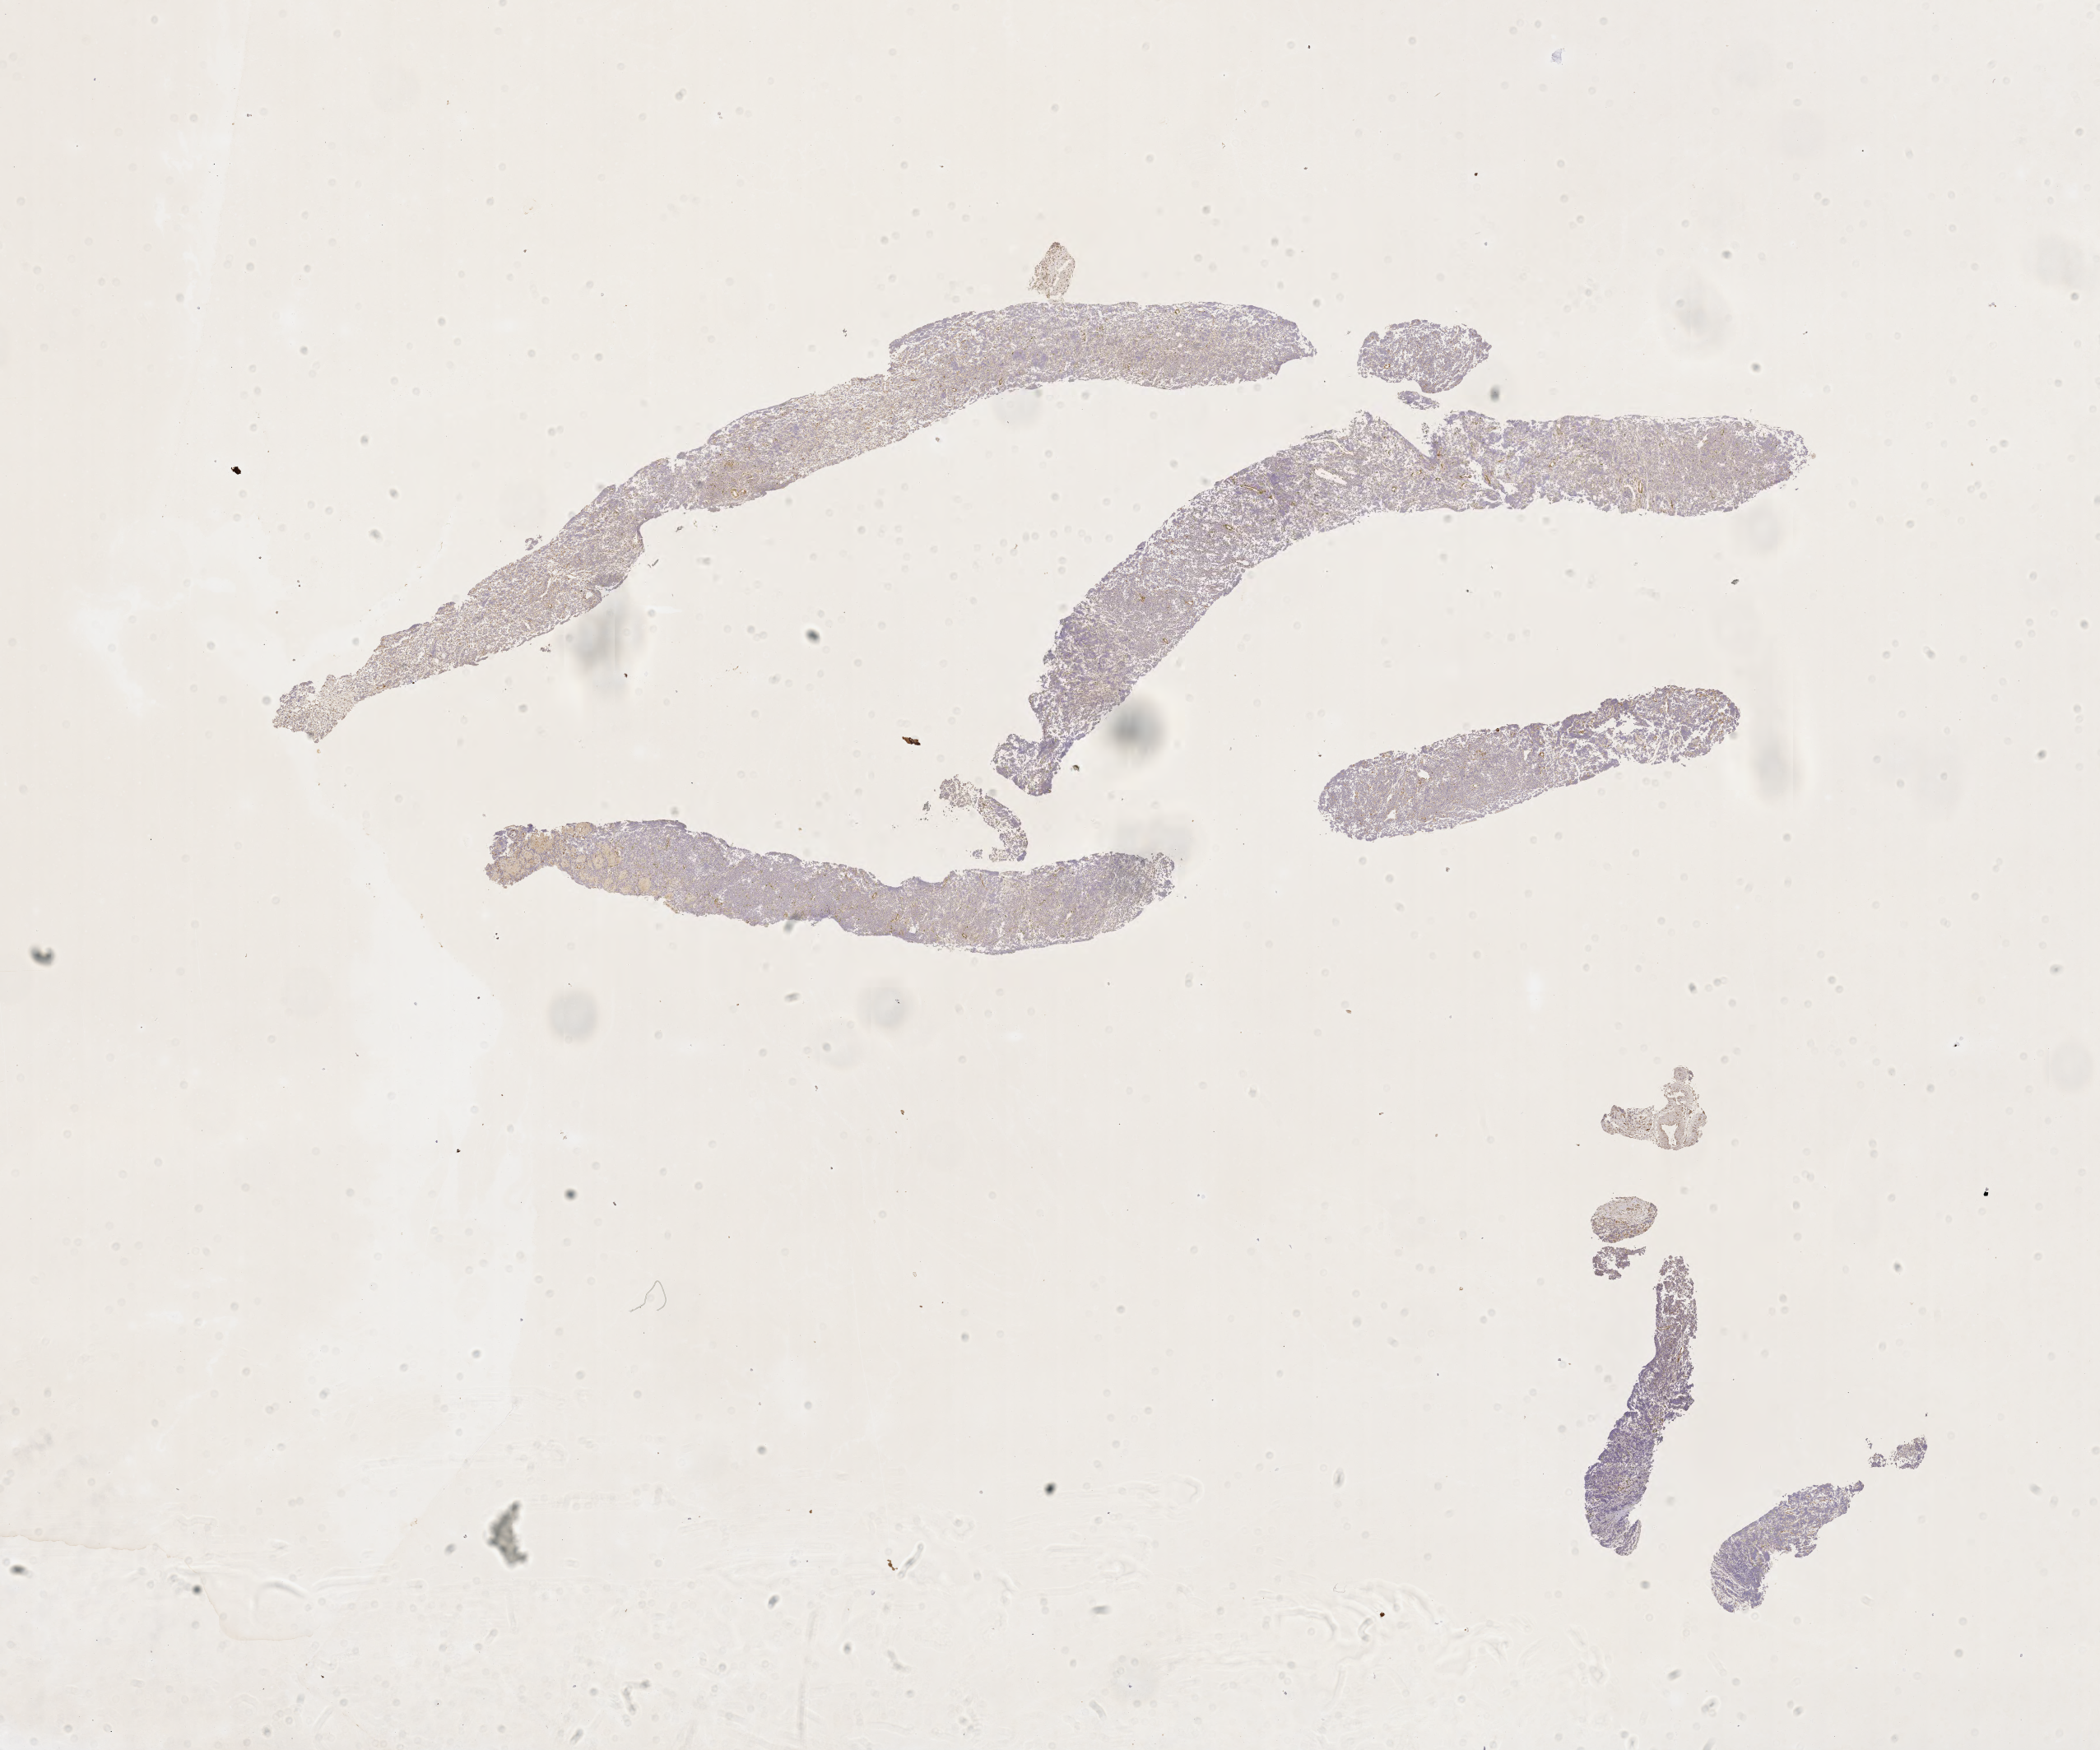
IHC for BCL2, whole-slide image — shown as a low-resolution overview of the whole scanned area (about 20.6 x 17.2 mm); tumor tissue. Male patient, 66 years old.
Histologic diagnosis: Burkitt lymphoma, NOS.